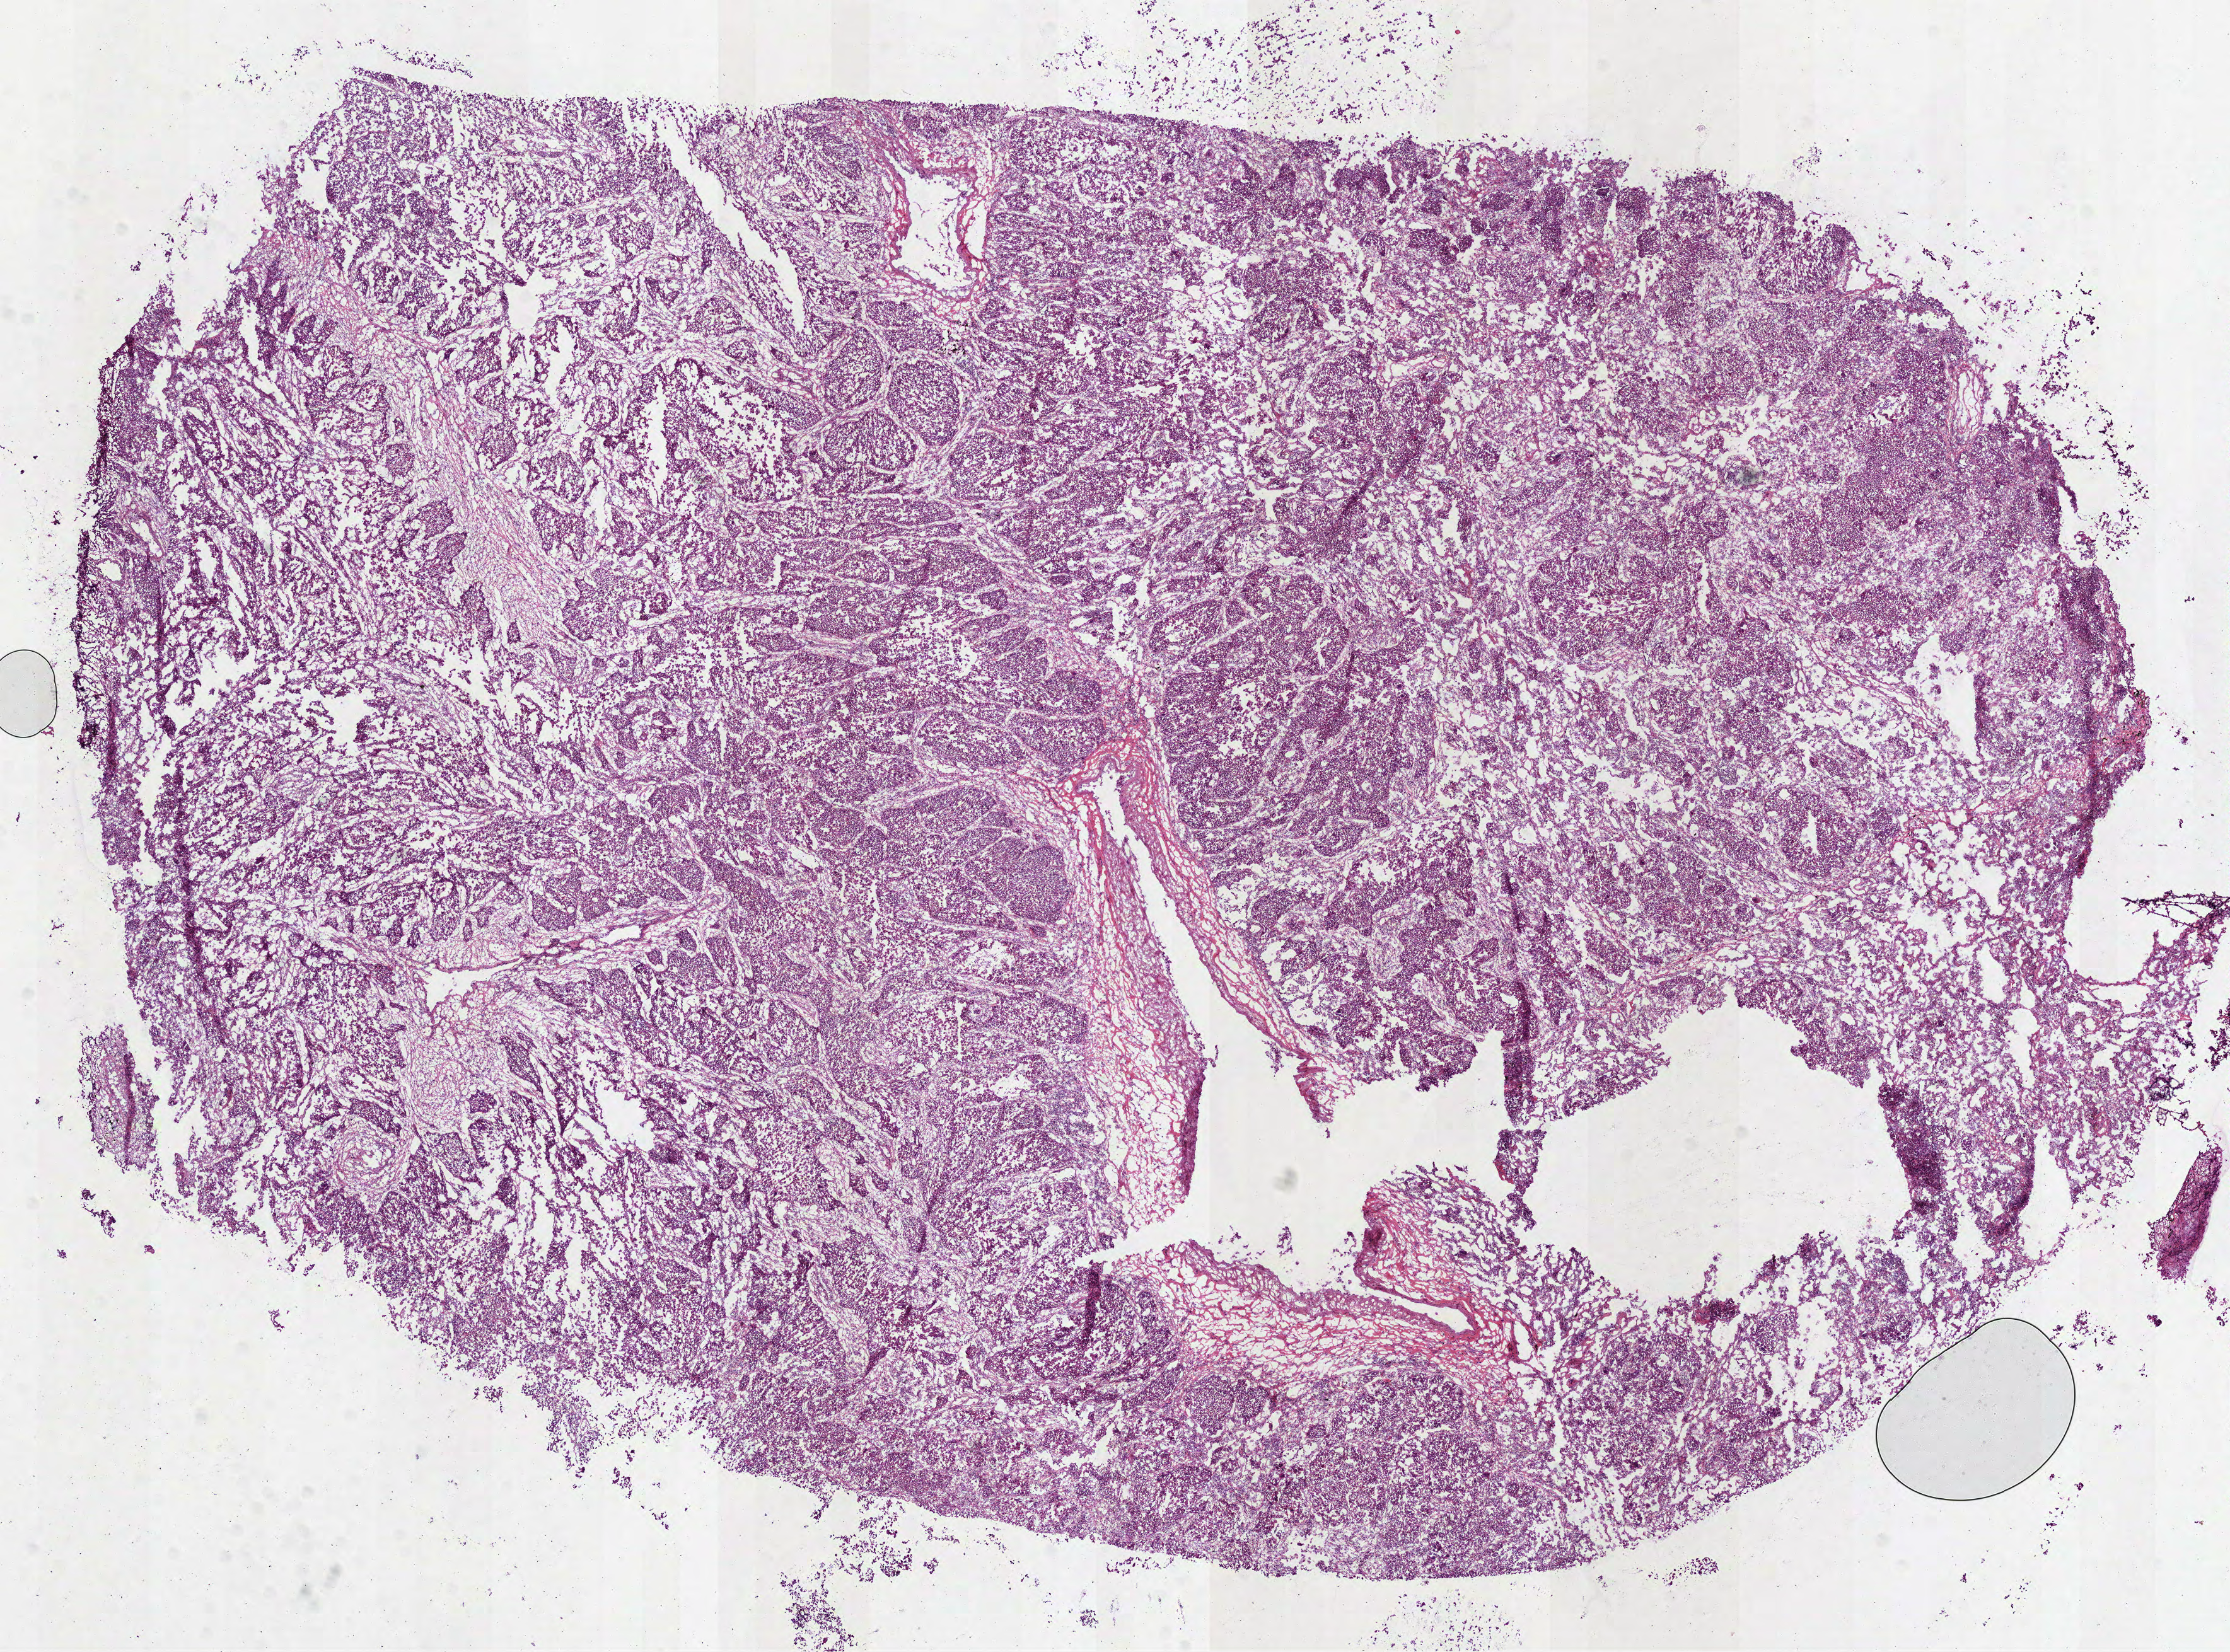
Whole-slide histology image, Hematoxylin and eosin (H&E) stained, shown as a low-resolution overview of the whole scanned area (about 14.3 x 10.6 mm); frozen section from the bottom of the tissue portion; primary tumour sample from the lung. Patient: male, age at initial diagnosis 67 years. Composition of this section per pathologist review: tumour cells 80%, tumour nuclei 75%, normal cells 5%, stromal cells 10%, necrosis 5%.
AJCC pathologic stage: IV (7th edition). Laterality: left. Diagnosis: Squamous cell carcinoma, NOS (upper lobe, lung). TNM: T4 N0 M1a.